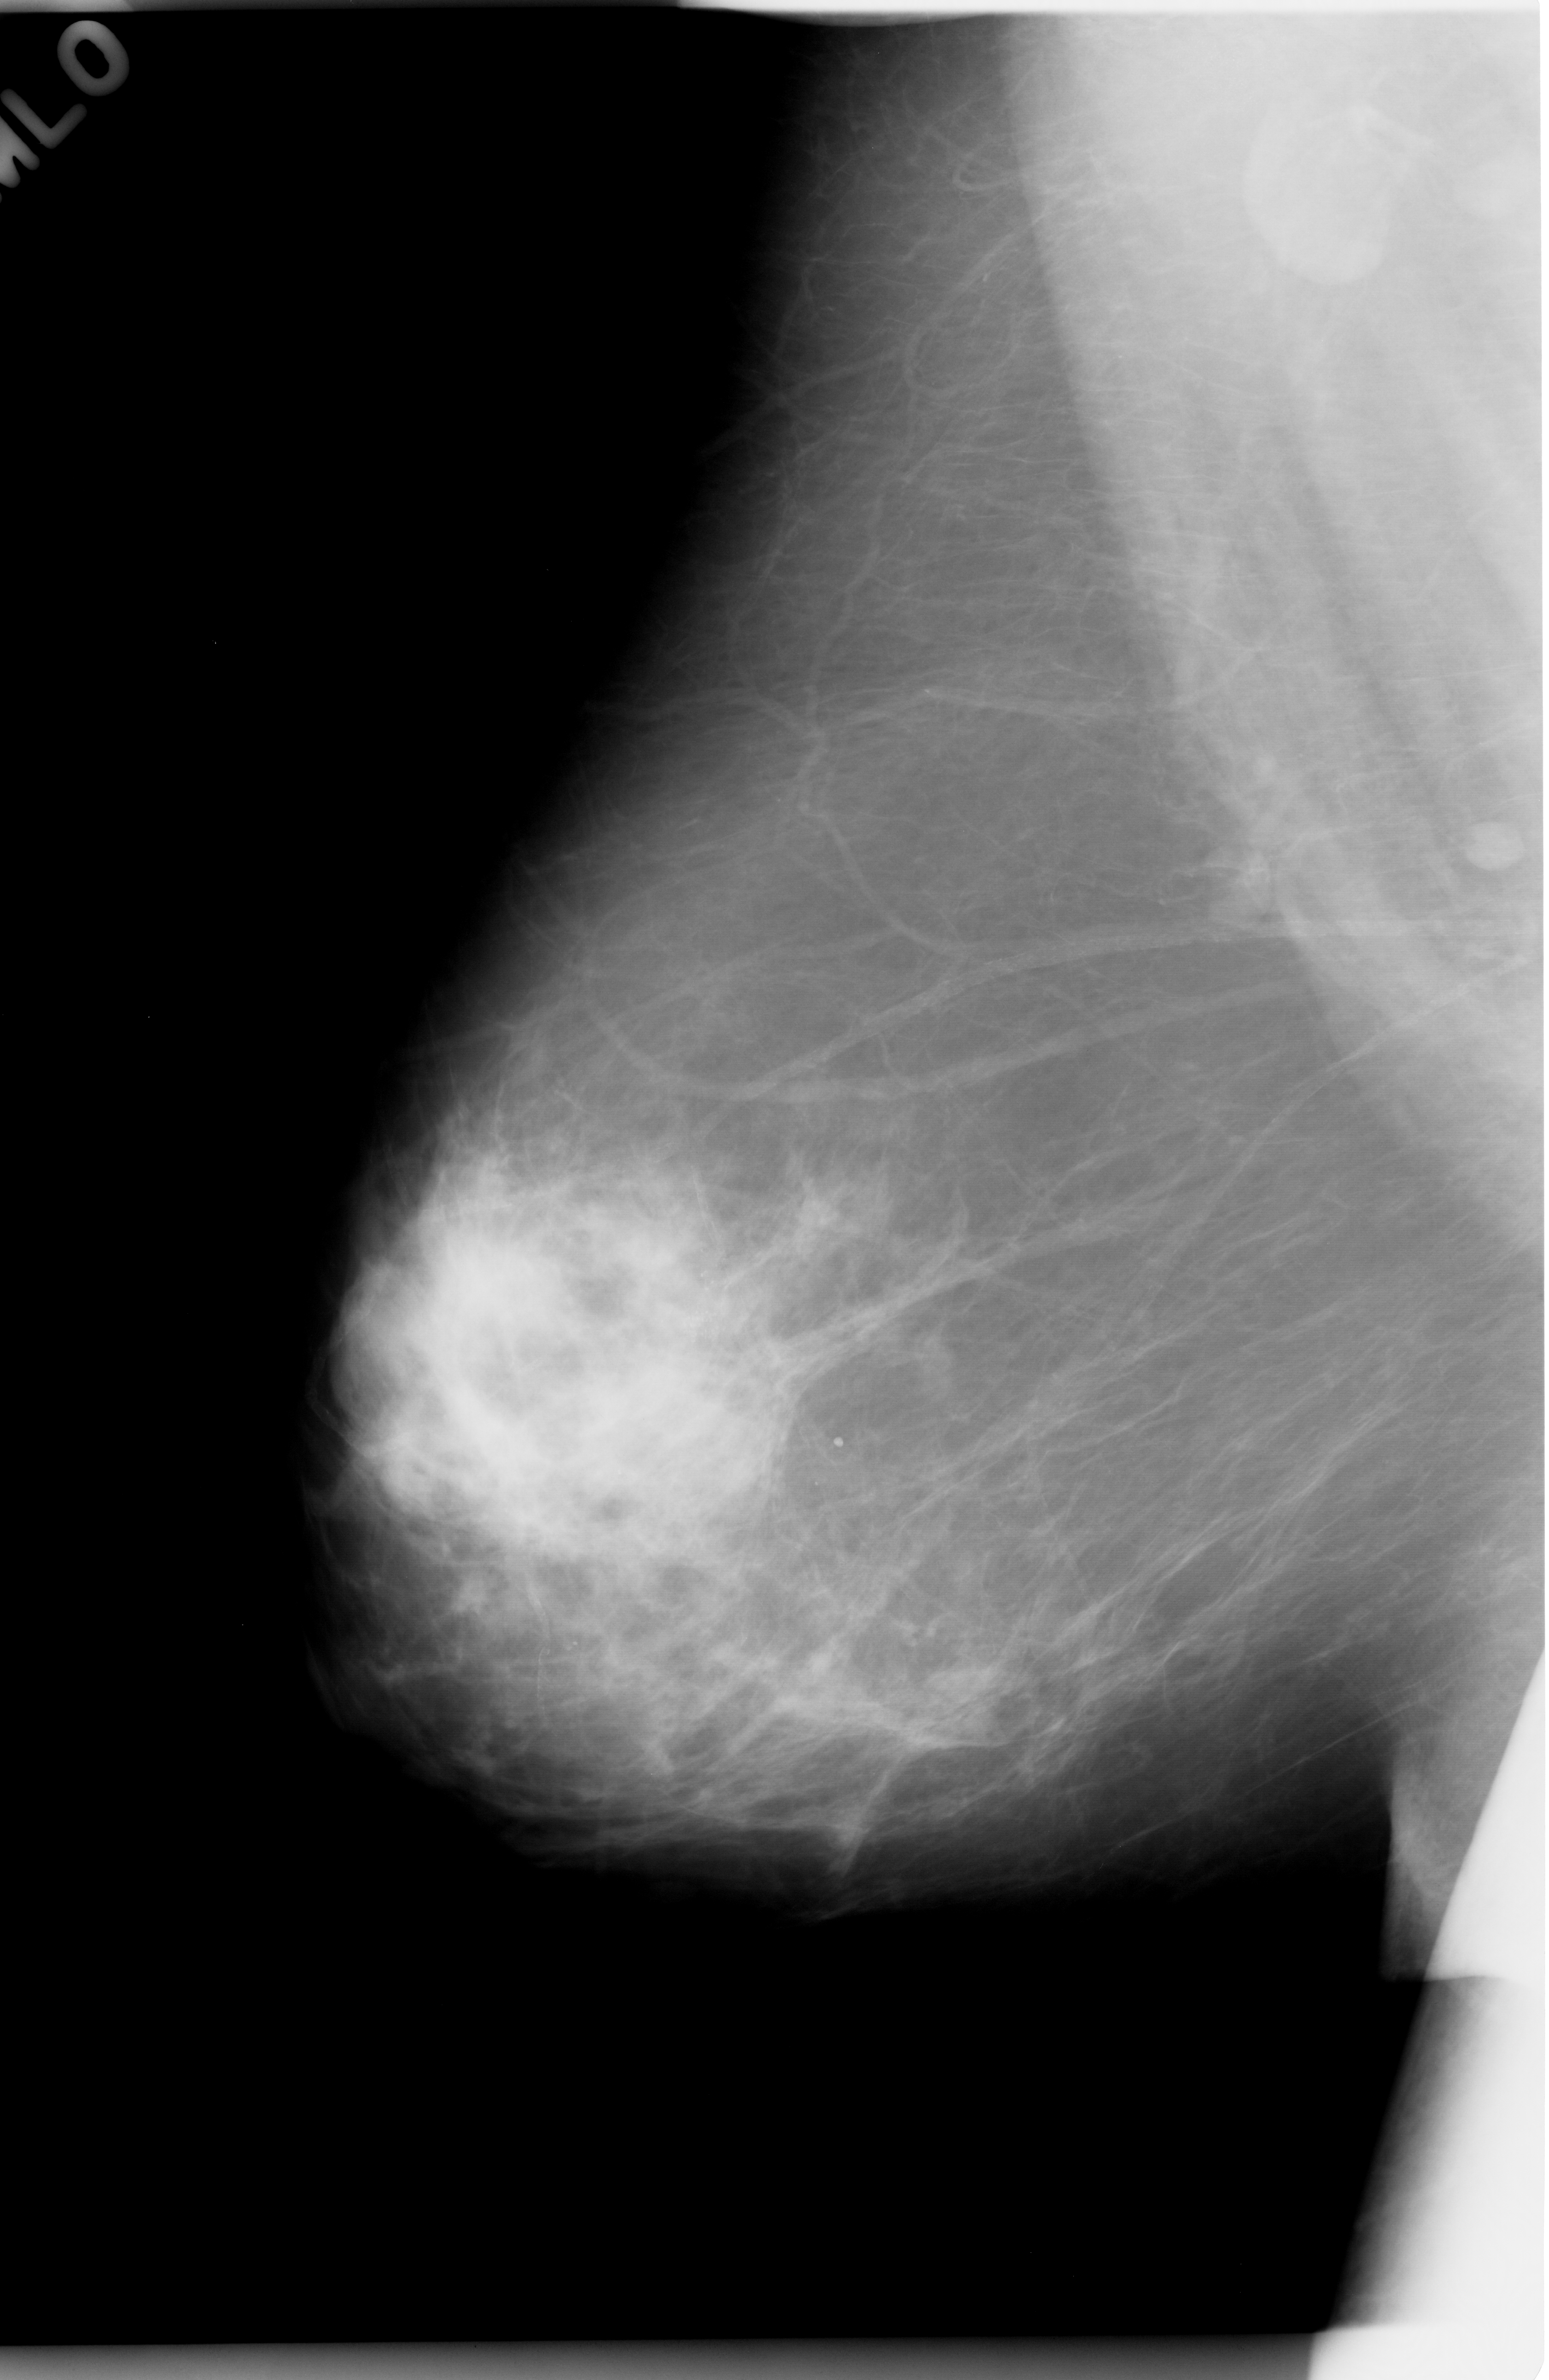
Mammogram (digitized film), right breast, MLO view, breast composition: scattered fibroglandular densities (BI-RADS density category 2 of 4).
Calcifications, morphology pleomorphic, distribution clustered; BI-RADS assessment category 5; subtlety rating 4 on a 1 (subtle) to 5 (obvious) scale; pathology (as recorded): malignant.